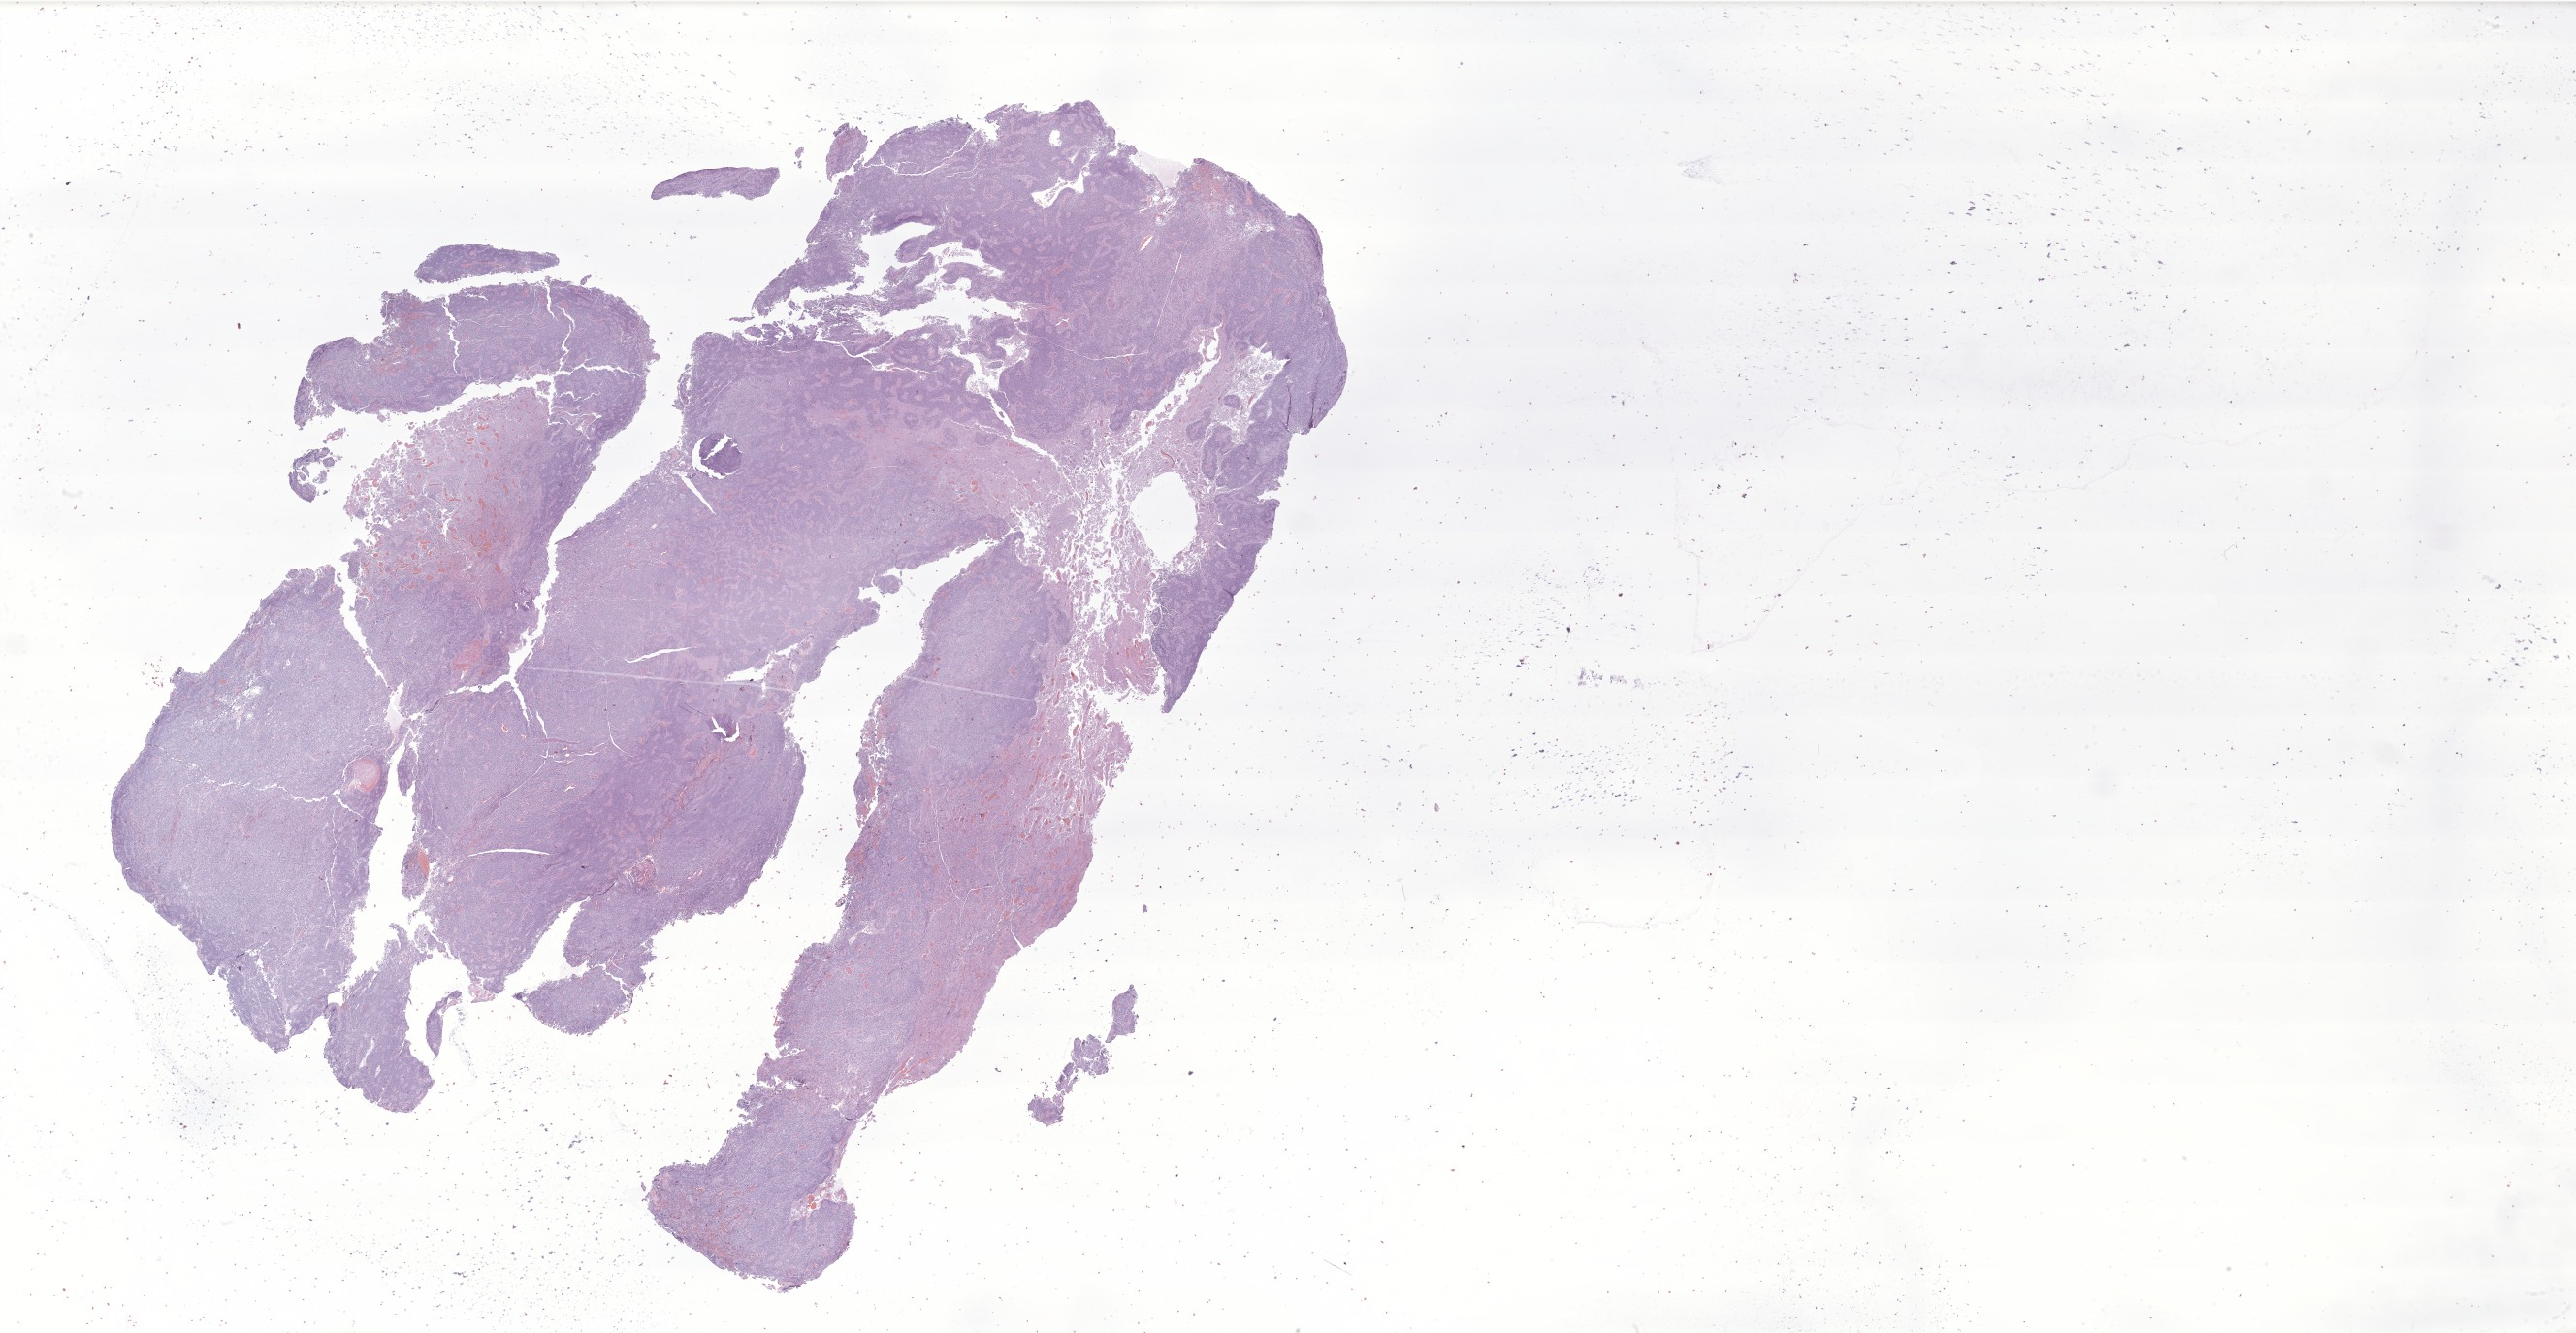
Digitized haematoxylin and eosin-stained section of tumor tissue from the frontal lobe — low-resolution overview of the scanned area, about 44.8 x 23.2 mm, FFPE section. Male patient, age 459 days (about 1.3 years).
Recorded diagnosis: Neoplasm, uncertain whether benign or malignant.